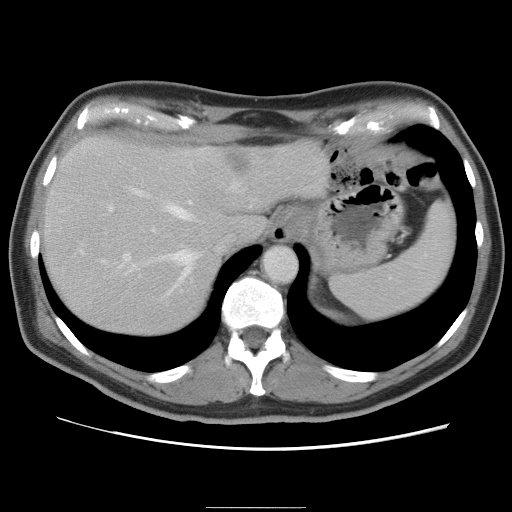
Contrast-enhanced abdominal CT, one axial slice. Slice 65 of 87 in the series (ordered by position). 120 kVp. Soft-tissue window (W 400 / L 40 HU). 512 × 512 image matrix, field of view 363 × 363 mm. Male patient, age 63 years. From the clinical record (not read from this slice): diagnosis: colorectal cancer liver metastases, imaged before liver resection; multiple liver metastases: no.
Outlined on this slice (expert manual segmentation):
- hepatic veins: bounding box <100,182,240,295> (left, top, right, bottom; pixels)
- liver: <41,138,329,336>
- planned liver remnant (the part of the liver to remain after resection): <41,162,218,336>
- portal vein (with intrahepatic branches): <106,203,167,275>
- liver metastasis: <228,155,249,172>